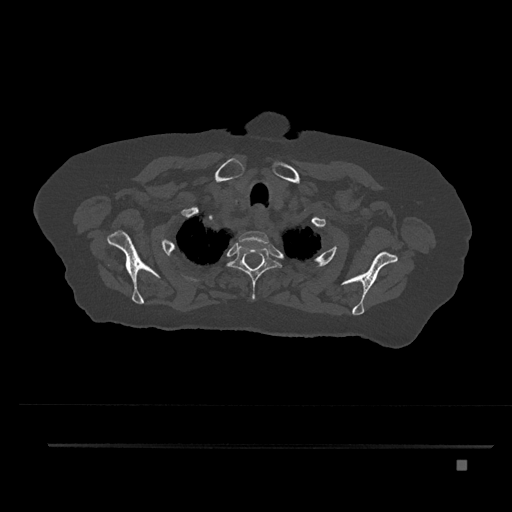
CT including the spine, one axial slice. Position 673 of 797 along the scan axis. Bone window (W 1800 / L 400 HU). 0.5 mm slice thickness. 512 × 512 image matrix, field of view 437 × 437 mm. Female patient, age 76 years. From the clinical record (not read from this slice): primary cancer: lung; vertebrae with lytic lesions (as recorded): T11, L3.
Outlined on this slice (semi-automatically segmented with operator editing):
- T1 vertebra: bounding box [x1, y1, x2, y2] px = [239, 231, 269, 247]
- T2 vertebra: [227, 243, 282, 300]